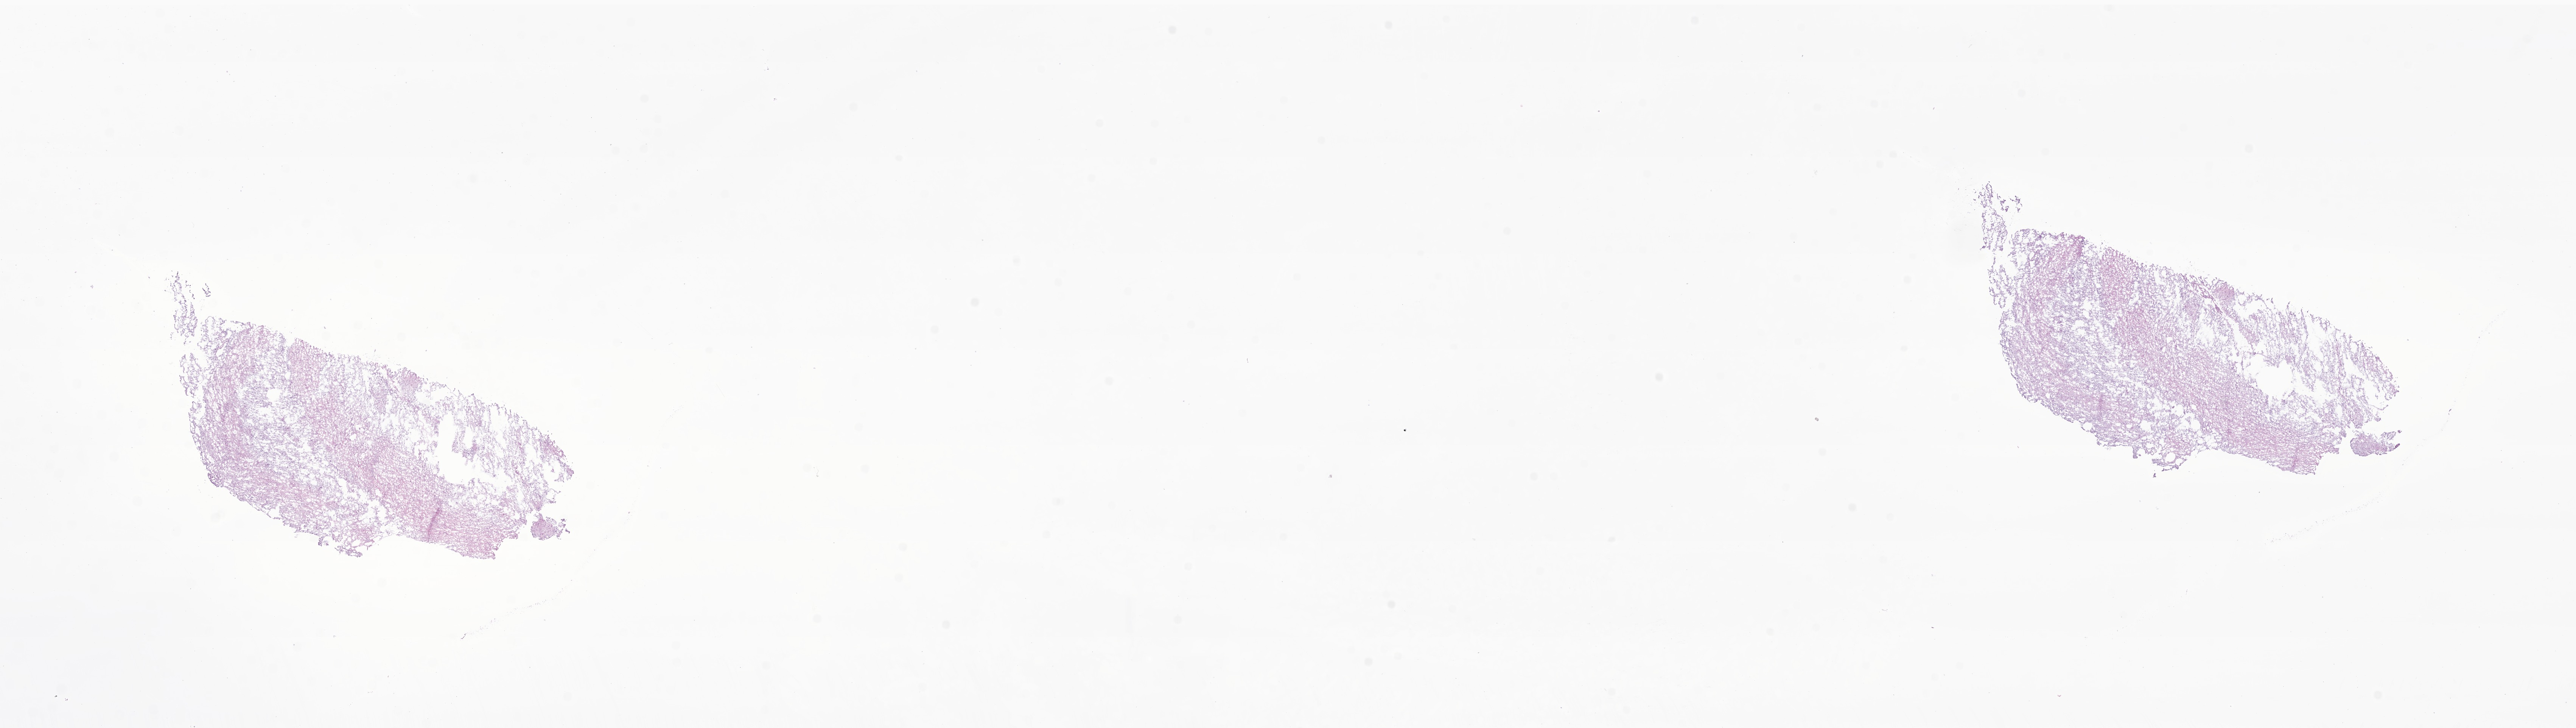
Whole-slide image, hematoxylin and eosin (H&E) stain of tumor tissue from the brain, a low-resolution overview of the entire scanned area, about 28.7 x 8.1 mm. Frozen section. Male patient, age 81 months (6 years 9 months).
- diagnosis (ICD-O-3 morphology term): Pilocytic astrocytoma